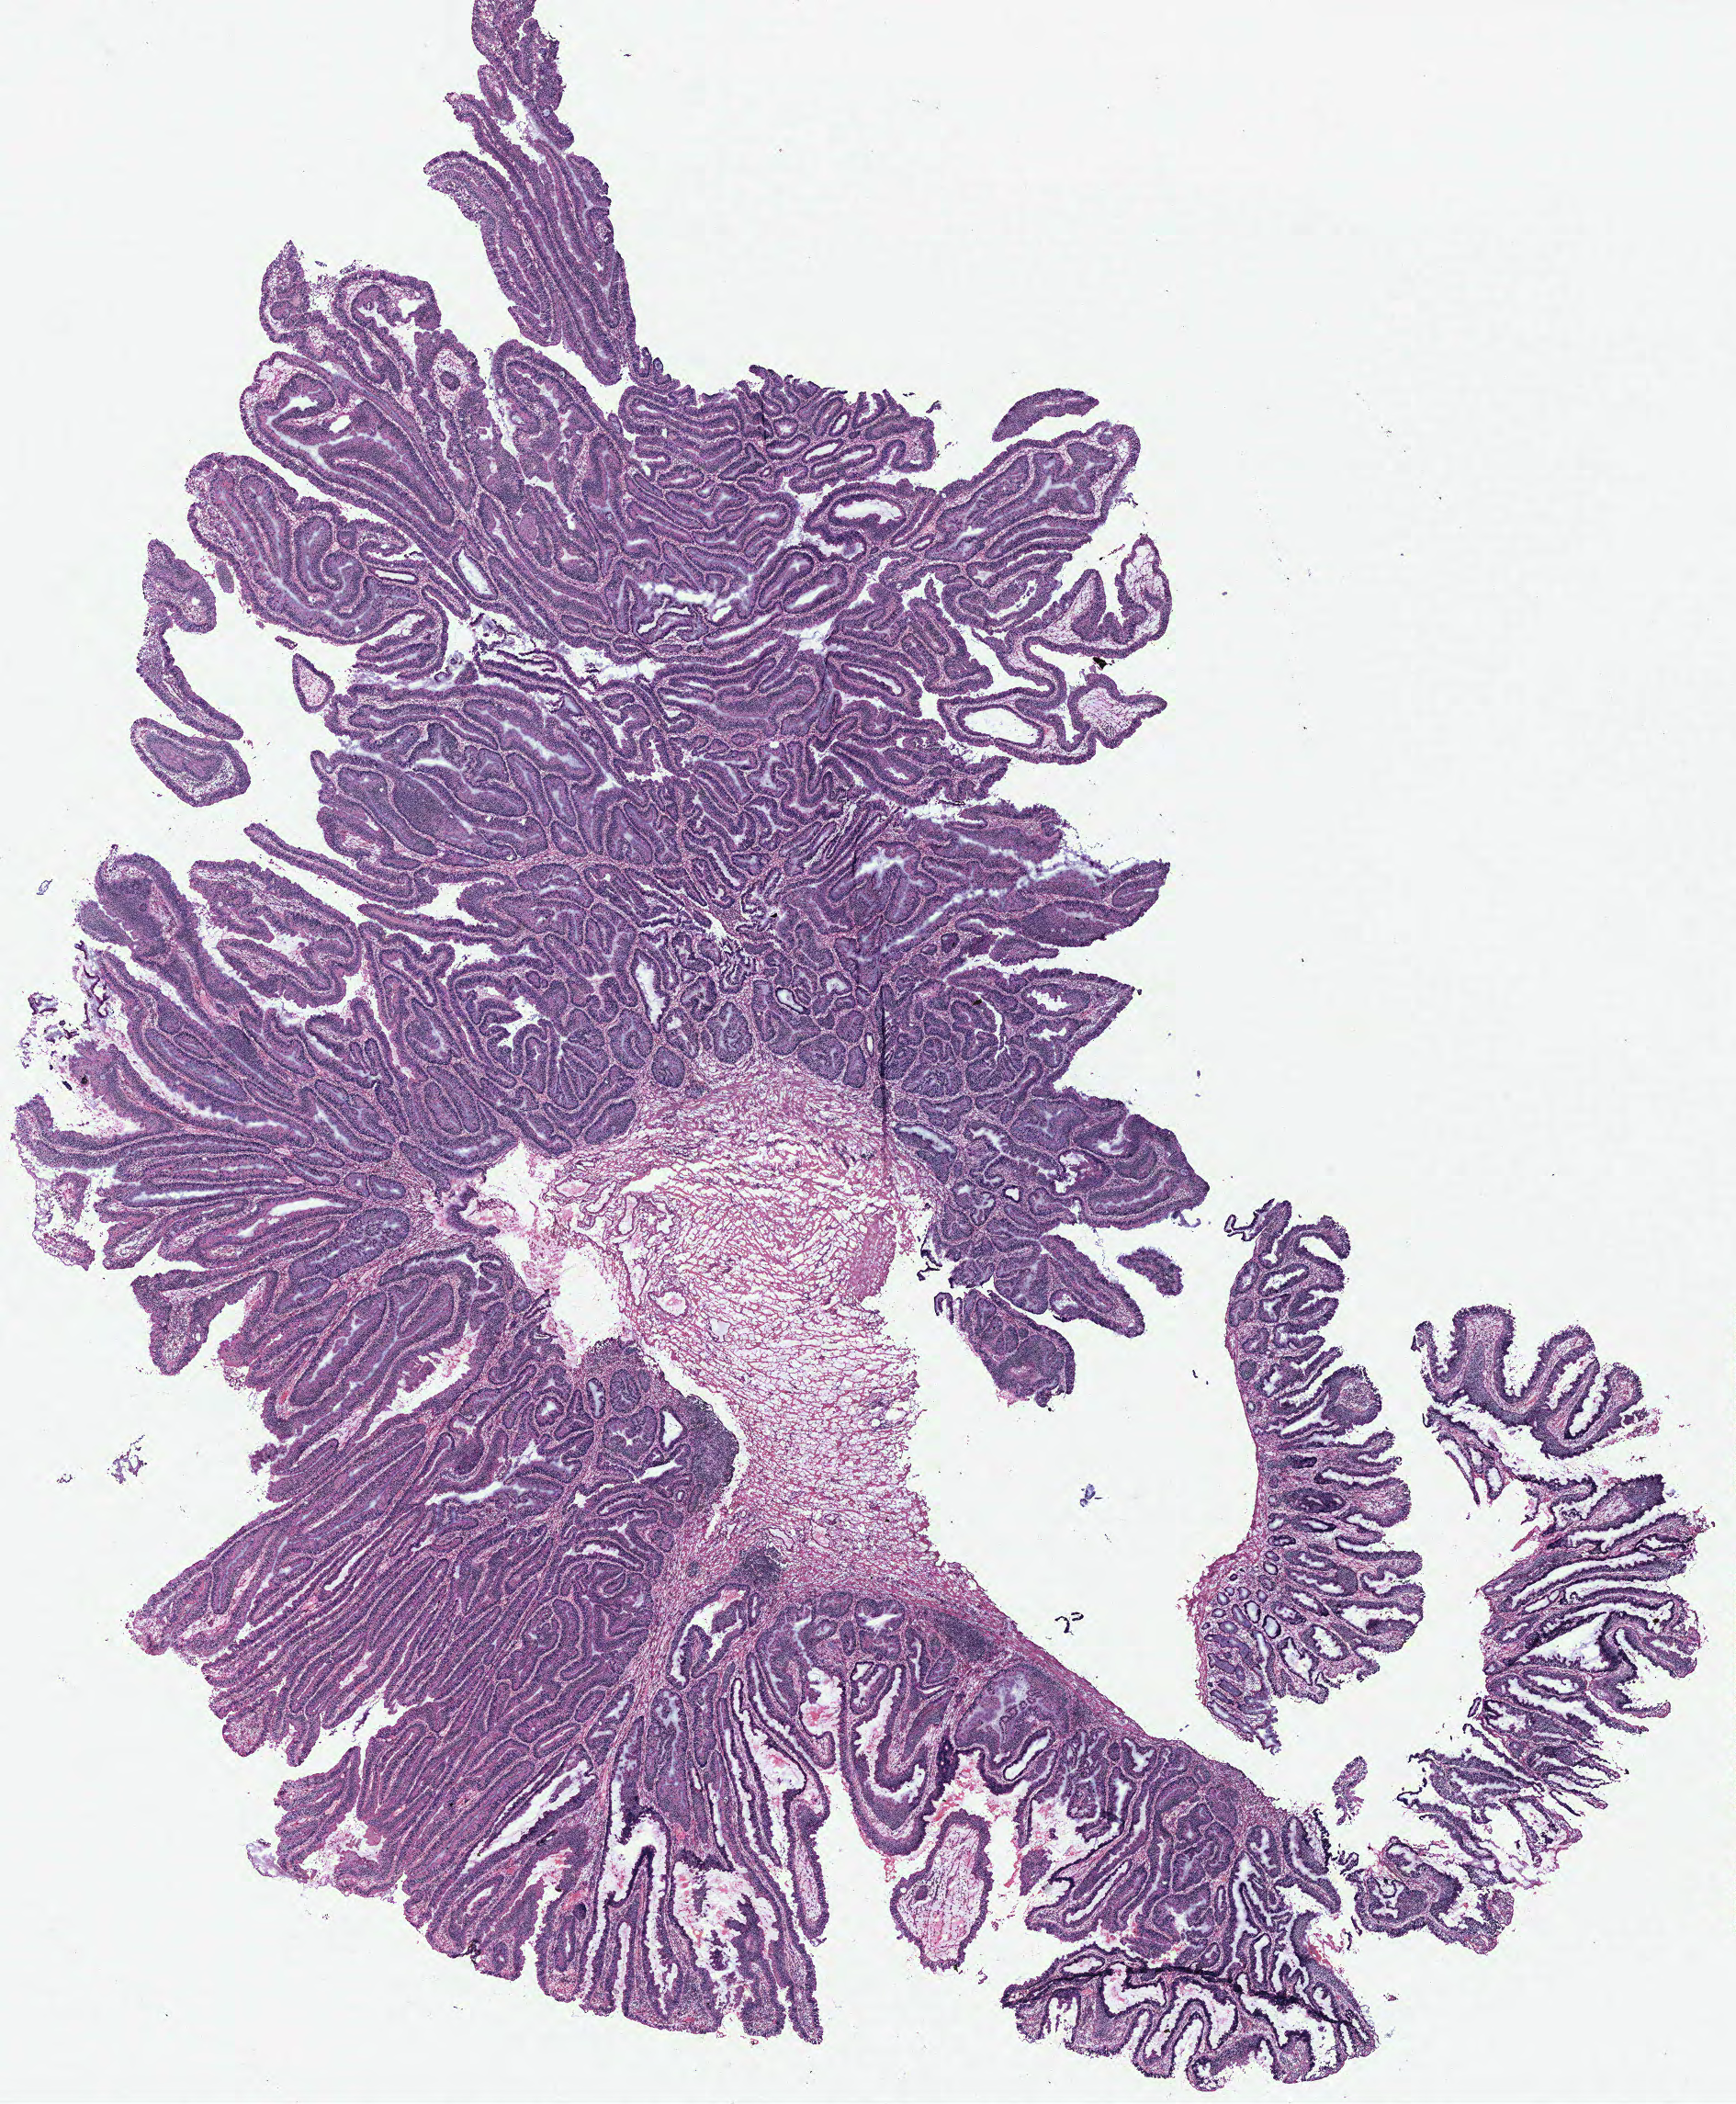
Digitized Hematoxylin and eosin (H&E) stained tissue section (whole slide), a low-resolution overview of the entire scanned area, about 15.1 x 18.3 mm, colon, normal (non-tumour) tissue. 57-year-old female patient.
This section: normal (non-tumour) tissue from the same patient. Patient diagnosis: Adenocarcinoma, NOS.